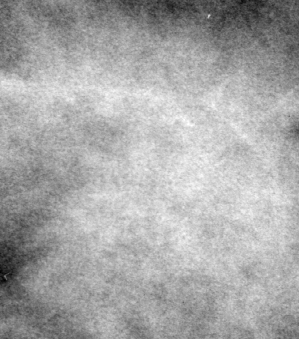
Region of interest cut from a scanned film mammogram (one marked finding); left breast; CC view; BI-RADS breast density category 4 (scale 1–4).
Mass, shape lobulated / architectural distortion, margins obscured / ill defined; BI-RADS assessment category 4; pathology result (as recorded, not read from the image): malignant.